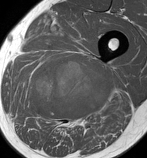
MRI of an extremity soft-tissue mass, one axial slice. Position 70 of 86 along the scan axis. MR volume resampled by the dataset authors to the PET/CT grid (not the native acquisition matrix). 3.27 mm slice thickness. 147 × 158 image matrix, field of view 144 × 154 mm. Male patient. Case-level facts recorded for this patient, not image findings: histological type: undifferentiated pleomorphic liposarcoma; grade: high; site of the primary tumour: left thigh.
Annotated regions visible in this slice (expert contour drawn on MRI and transferred to this co-registered scan by the dataset authors):
- gross tumour volume including surrounding oedema: bounding box (x1, y1, x2, y2) in pixels: (21, 56, 115, 127)
- gross tumour volume (mass): (30, 58, 113, 118)